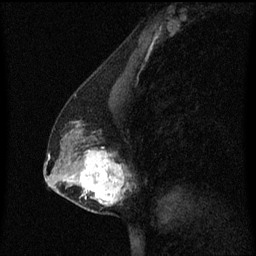
Breast MRI (dynamic contrast-enhanced), one sagittal slice; slice 29 of 60 in the series (ordered by position); dynamic contrast-enhanced series, image 2 of 3 at this slice position (ordered by acquisition); 1.5 T; TE 4.2 ms, TR 8.4 ms; 2 mm slice thickness; 256 × 256 image matrix, field of view 200 × 200 mm. Patient: female, 40 years. From the clinical record (not read from this slice): setting: breast cancer imaged before/during neoadjuvant chemotherapy; receptor status: triple-negative.
Structures marked on this image (semi-automatic segmentation, software-assisted and operator-edited):
- analysis volume of interest (the breast-tissue region the enhancement analysis was run in; not a lesion): bounding box [x1, y1, x2, y2] px = [60, 120, 133, 215]
- tumour enhancement mask (voxels above the 70 % enhancement threshold inside the analysis volume of interest): [62, 150, 125, 205]